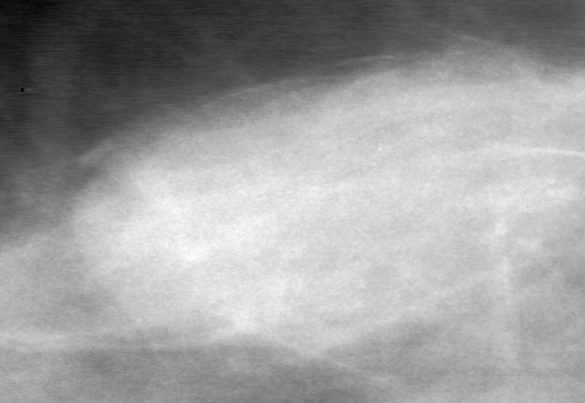
Cropped region of a digitized screen-film mammogram centred on a radiologist-marked abnormality; right breast; CC view; BI-RADS breast density category 3 (scale 1–4).
Finding: mass, shape oval, margins obscured; BI-RADS assessment category 0; pathology result (as recorded, not read from the image): benign.